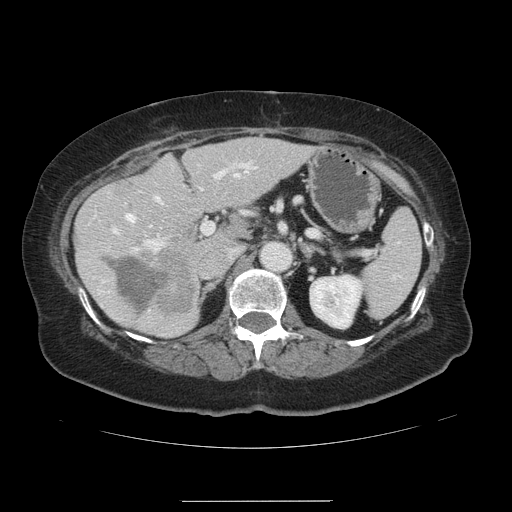
Contrast-enhanced abdominal CT, one axial slice; position 74 of 141 along the scan axis; intravenous contrast given; soft-tissue window (W 400 / L 40 HU); 2.5 mm slice thickness; 512 × 512 image matrix, field of view 393 × 393 mm. Female patient, age 74 years. From the clinical record (not read from this slice): diagnosis: colorectal cancer liver metastases, imaged before liver resection; multiple liver metastases: yes; largest metastasis: 7 cm; disease in both lobes: yes.
Structures marked on this image (outlined manually by an expert reader):
- hepatic veins: bounding box (x1, y1, x2, y2) in pixels: (126, 173, 238, 228)
- liver: (75, 138, 310, 337)
- planned liver remnant (the part of the liver to remain after resection): (83, 138, 310, 337)
- portal vein (with intrahepatic branches): (112, 162, 250, 252)
- liver metastasis: (110, 259, 169, 314)
- liver metastasis: (158, 248, 194, 312)